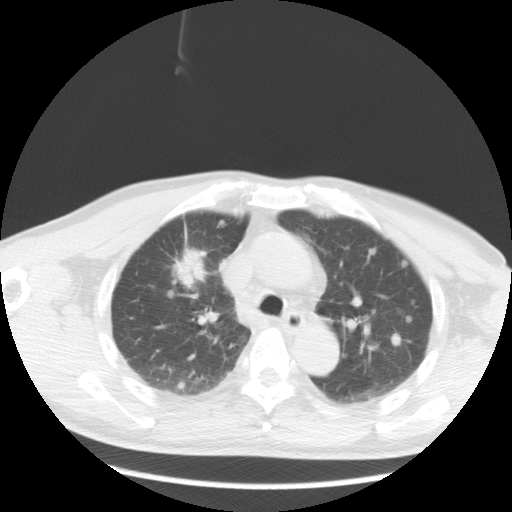
Chest CT, one axial slice; reconstruction kernel STANDARD; lung window (W 1500 / L -600 HU); 512 × 512 image matrix, field of view 369 × 369 mm. Male patient, age 57 years. From the clinical record (not read from this slice): clinical TNM (as recorded): T2 N3 M1a.
Annotated regions visible in this slice (bounding box drawn by a radiologist):
- lung tumour (recorded histology: adenocarcinoma): bounding box <170,248,207,292> (left, top, right, bottom; pixels)